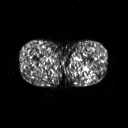
FDG PET of an extremity soft-tissue mass (from a PET/CT study), one axial slice. Slice 232 of 267 in the series (ordered by position). 3.27 mm slice thickness. 128 × 128 image matrix, field of view 500 × 500 mm. Male patient, age 27 years. Case-level facts recorded for this patient, not image findings: histological type: extraskeletal osteosarcoma; grade: high; site of the primary tumour: left adductur.
Structures marked on this image (expert contour drawn on MRI and transferred to this co-registered scan by the dataset authors):
- gross tumour volume (mass): bounding box [x1, y1, x2, y2] px = [67, 60, 93, 76]